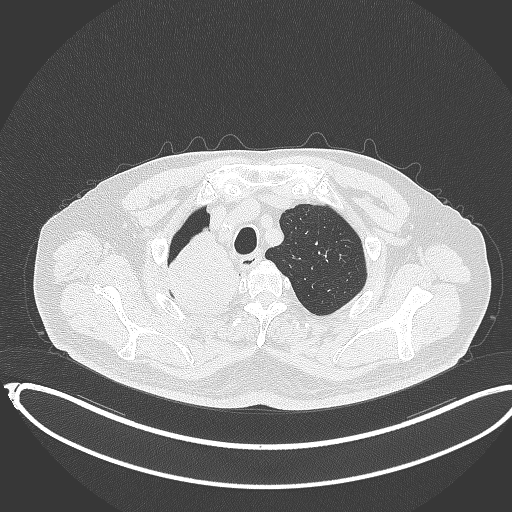
Chest CT, one axial slice. Slice 316 of 403 in the series (ordered by position). 120 kVp. Lung window (W 1500 / L -600 HU). 512 × 512 image matrix. Patient: male, 68 years. From the clinical record (not read from this slice): clinical TNM (as recorded): T2a N0 M0.
Outlined on this slice (bounding box drawn by a radiologist):
- lung tumour (recorded histology: adenocarcinoma): bounding box (x1, y1, x2, y2) in pixels: (161, 231, 245, 315)